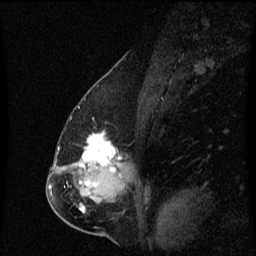
Breast MRI (dynamic contrast-enhanced), one sagittal slice. Position 34 of 60 along the scan axis. Dynamic contrast-enhanced series, image 2 of 3 at this slice position (ordered by acquisition). 1.5 T. TE 4.2 ms, TR 8.4 ms. 2 mm slice thickness. 256 × 256 image matrix. Patient: female, 57 years. Case-level facts recorded for this patient, not image findings: setting: breast cancer imaged before/during neoadjuvant chemotherapy; receptor status: HR-positive, HER2-negative.
Outlined on this slice (semi-automatically segmented with operator editing):
- analysis volume of interest (the breast-tissue region the enhancement analysis was run in; not a lesion): box from (x=66, y=132) to (x=129, y=177) px
- tumour enhancement mask (voxels above the 70 % enhancement threshold inside the analysis volume of interest): (x=80, y=132)–(x=121, y=177)